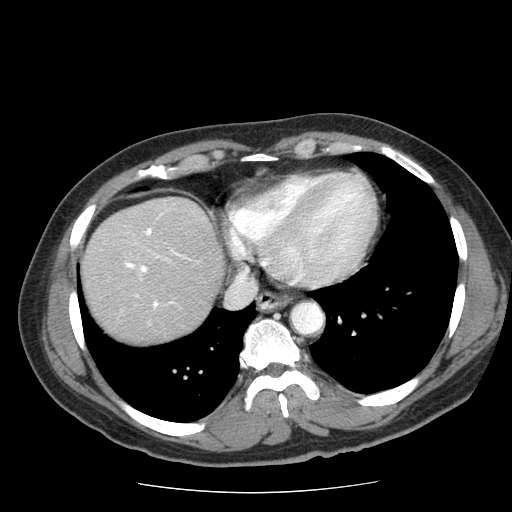
Contrast-enhanced abdominal CT (liver protocol), one axial slice. Position 63 of 85 along the scan axis. Soft-tissue window (W 400 / L 40 HU). 2.5 mm slice thickness. 512 × 512 image matrix, field of view 360 × 360 mm. Case-level facts recorded for this patient, not image findings: diagnosis: hepatocellular carcinoma (patient treated with transarterial chemoembolisation; whether this scan precedes or follows treatment is not stated here); TNM stage (as recorded): Stage-IIIA.
Outlined on this slice (semi-automatically segmented with operator editing):
- liver parenchyma outside the tumour (the mass and vessels are separate outlines, so this box may not span the whole liver): bounding box <82,196,224,342> (left, top, right, bottom; pixels)
- liver vessels: <125,228,191,308>